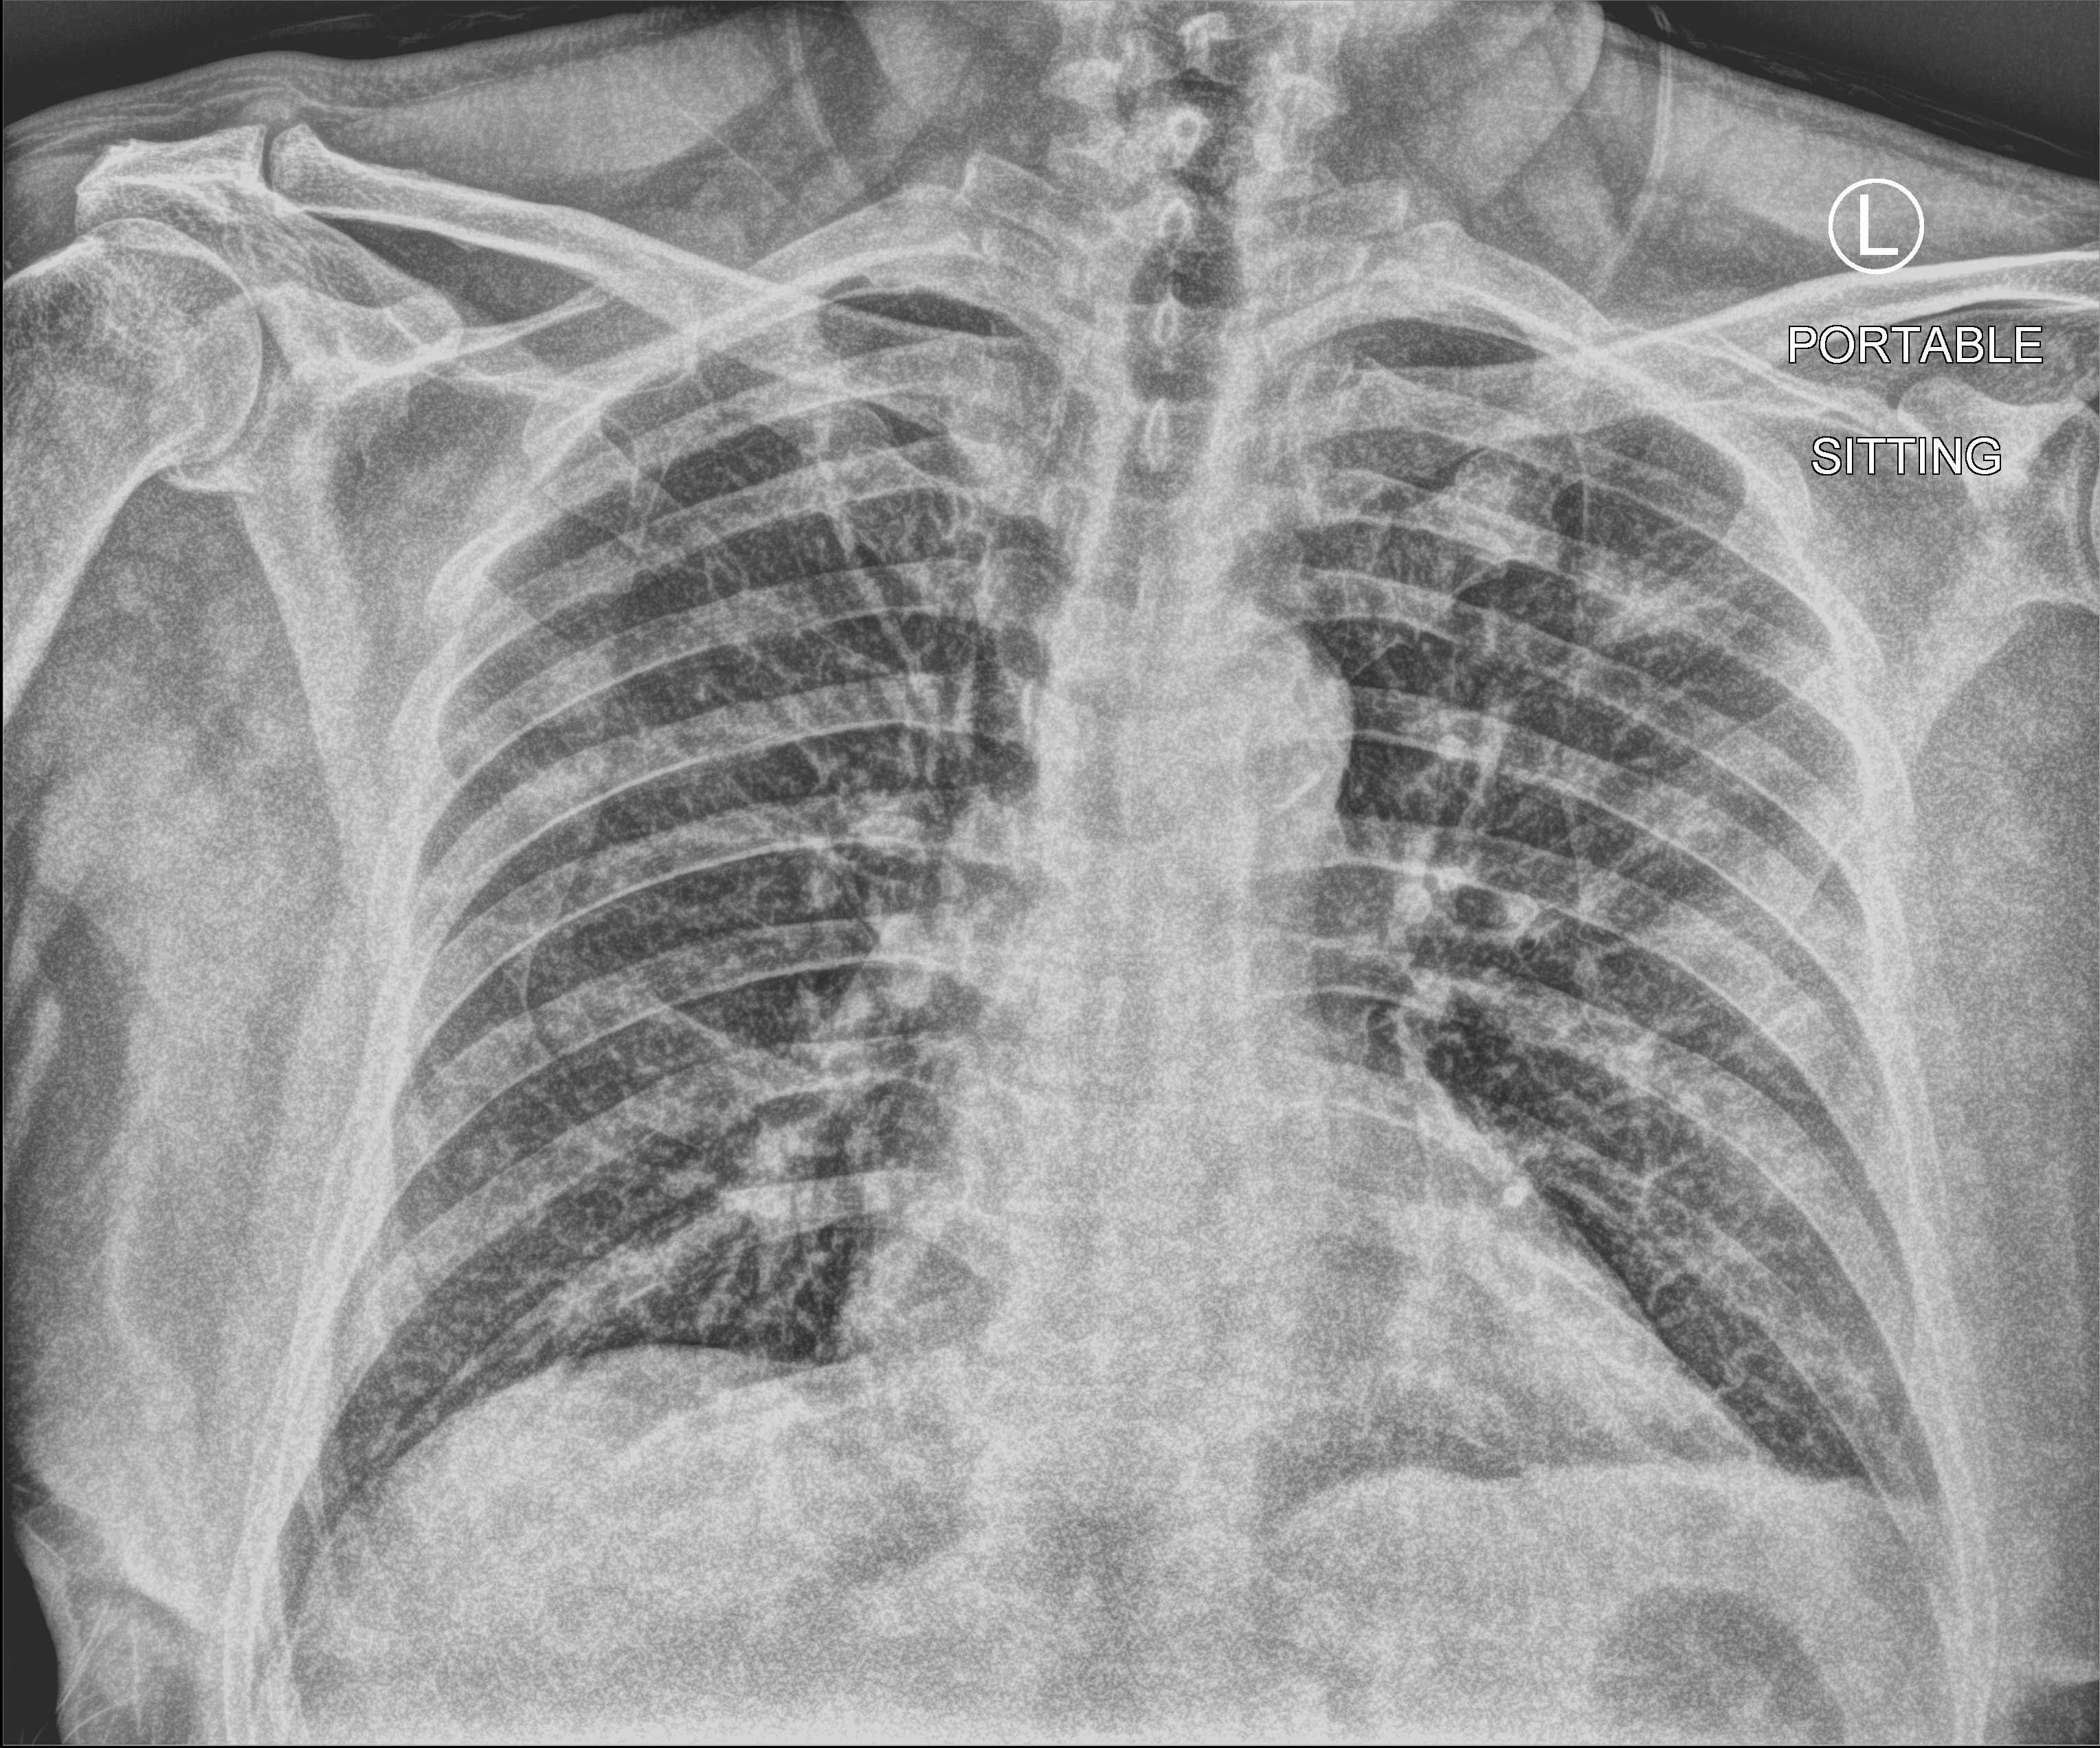
Portable chest radiograph, anteroposterior (AP) projection. Male patient hospitalised with COVID-19, age 60–74 years.
Admission-level facts for this patient (not findings on this image; timing relative to this image not recorded): mechanically ventilated during this hospital stay: no.